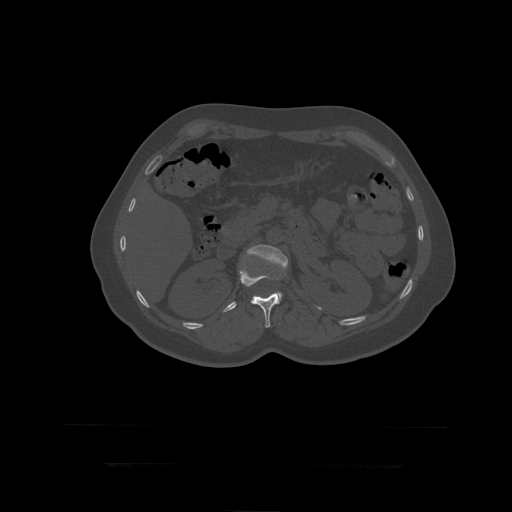
CT including the spine, one axial slice. Bone window (W 1800 / L 400 HU). 1.25 mm slice thickness. 512 × 512 image matrix. Patient age 41 years. From the clinical record (not read from this slice): primary cancer: breast.
Annotated regions visible in this slice (semi-automatic segmentation, software-assisted and operator-edited):
- L1 vertebra: box from (x=240, y=267) to (x=280, y=328) px
- L2 vertebra: (x=247, y=245)–(x=288, y=301)